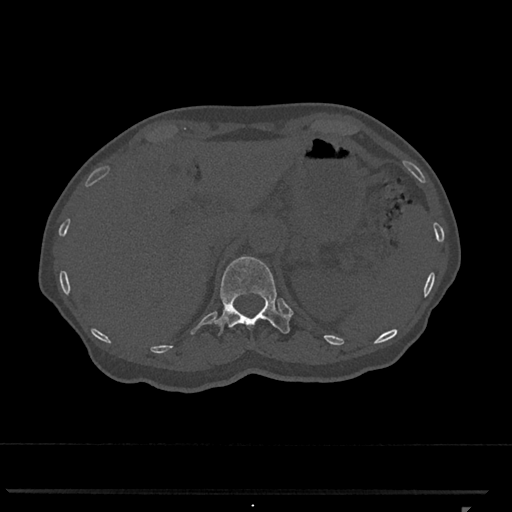
CT including the spine, one axial slice. Position 464 of 793 along the scan axis. Reconstruction kernel Br40s/3. 120 kVp. Bone window (W 1800 / L 400 HU). 512 × 512 image matrix, field of view 380 × 380 mm. Patient: female, 62 years. From the clinical record (not read from this slice): primary cancer: renal.
Structures marked on this image (semi-automatically segmented with operator editing):
- T12 vertebra: bounding box <212,256,290,335> (left, top, right, bottom; pixels)